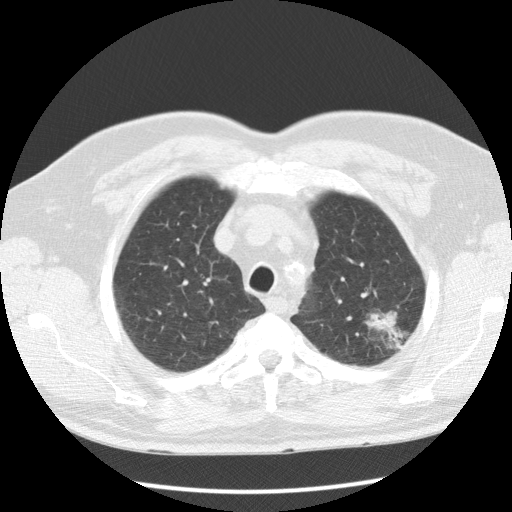
Low-dose screening chest CT, one axial slice; position 101 of 123 along the scan axis; reconstruction kernel STANDARD; lung window (W 1500 / L -600 HU); 512 × 512 image matrix, field of view 355 × 355 mm.
Annotated regions visible in this slice (outlined manually by an expert reader):
- lesion 1 (tumor, upper lobe of left lung): bounding box [x1, y1, x2, y2] px = [372, 309, 396, 332]